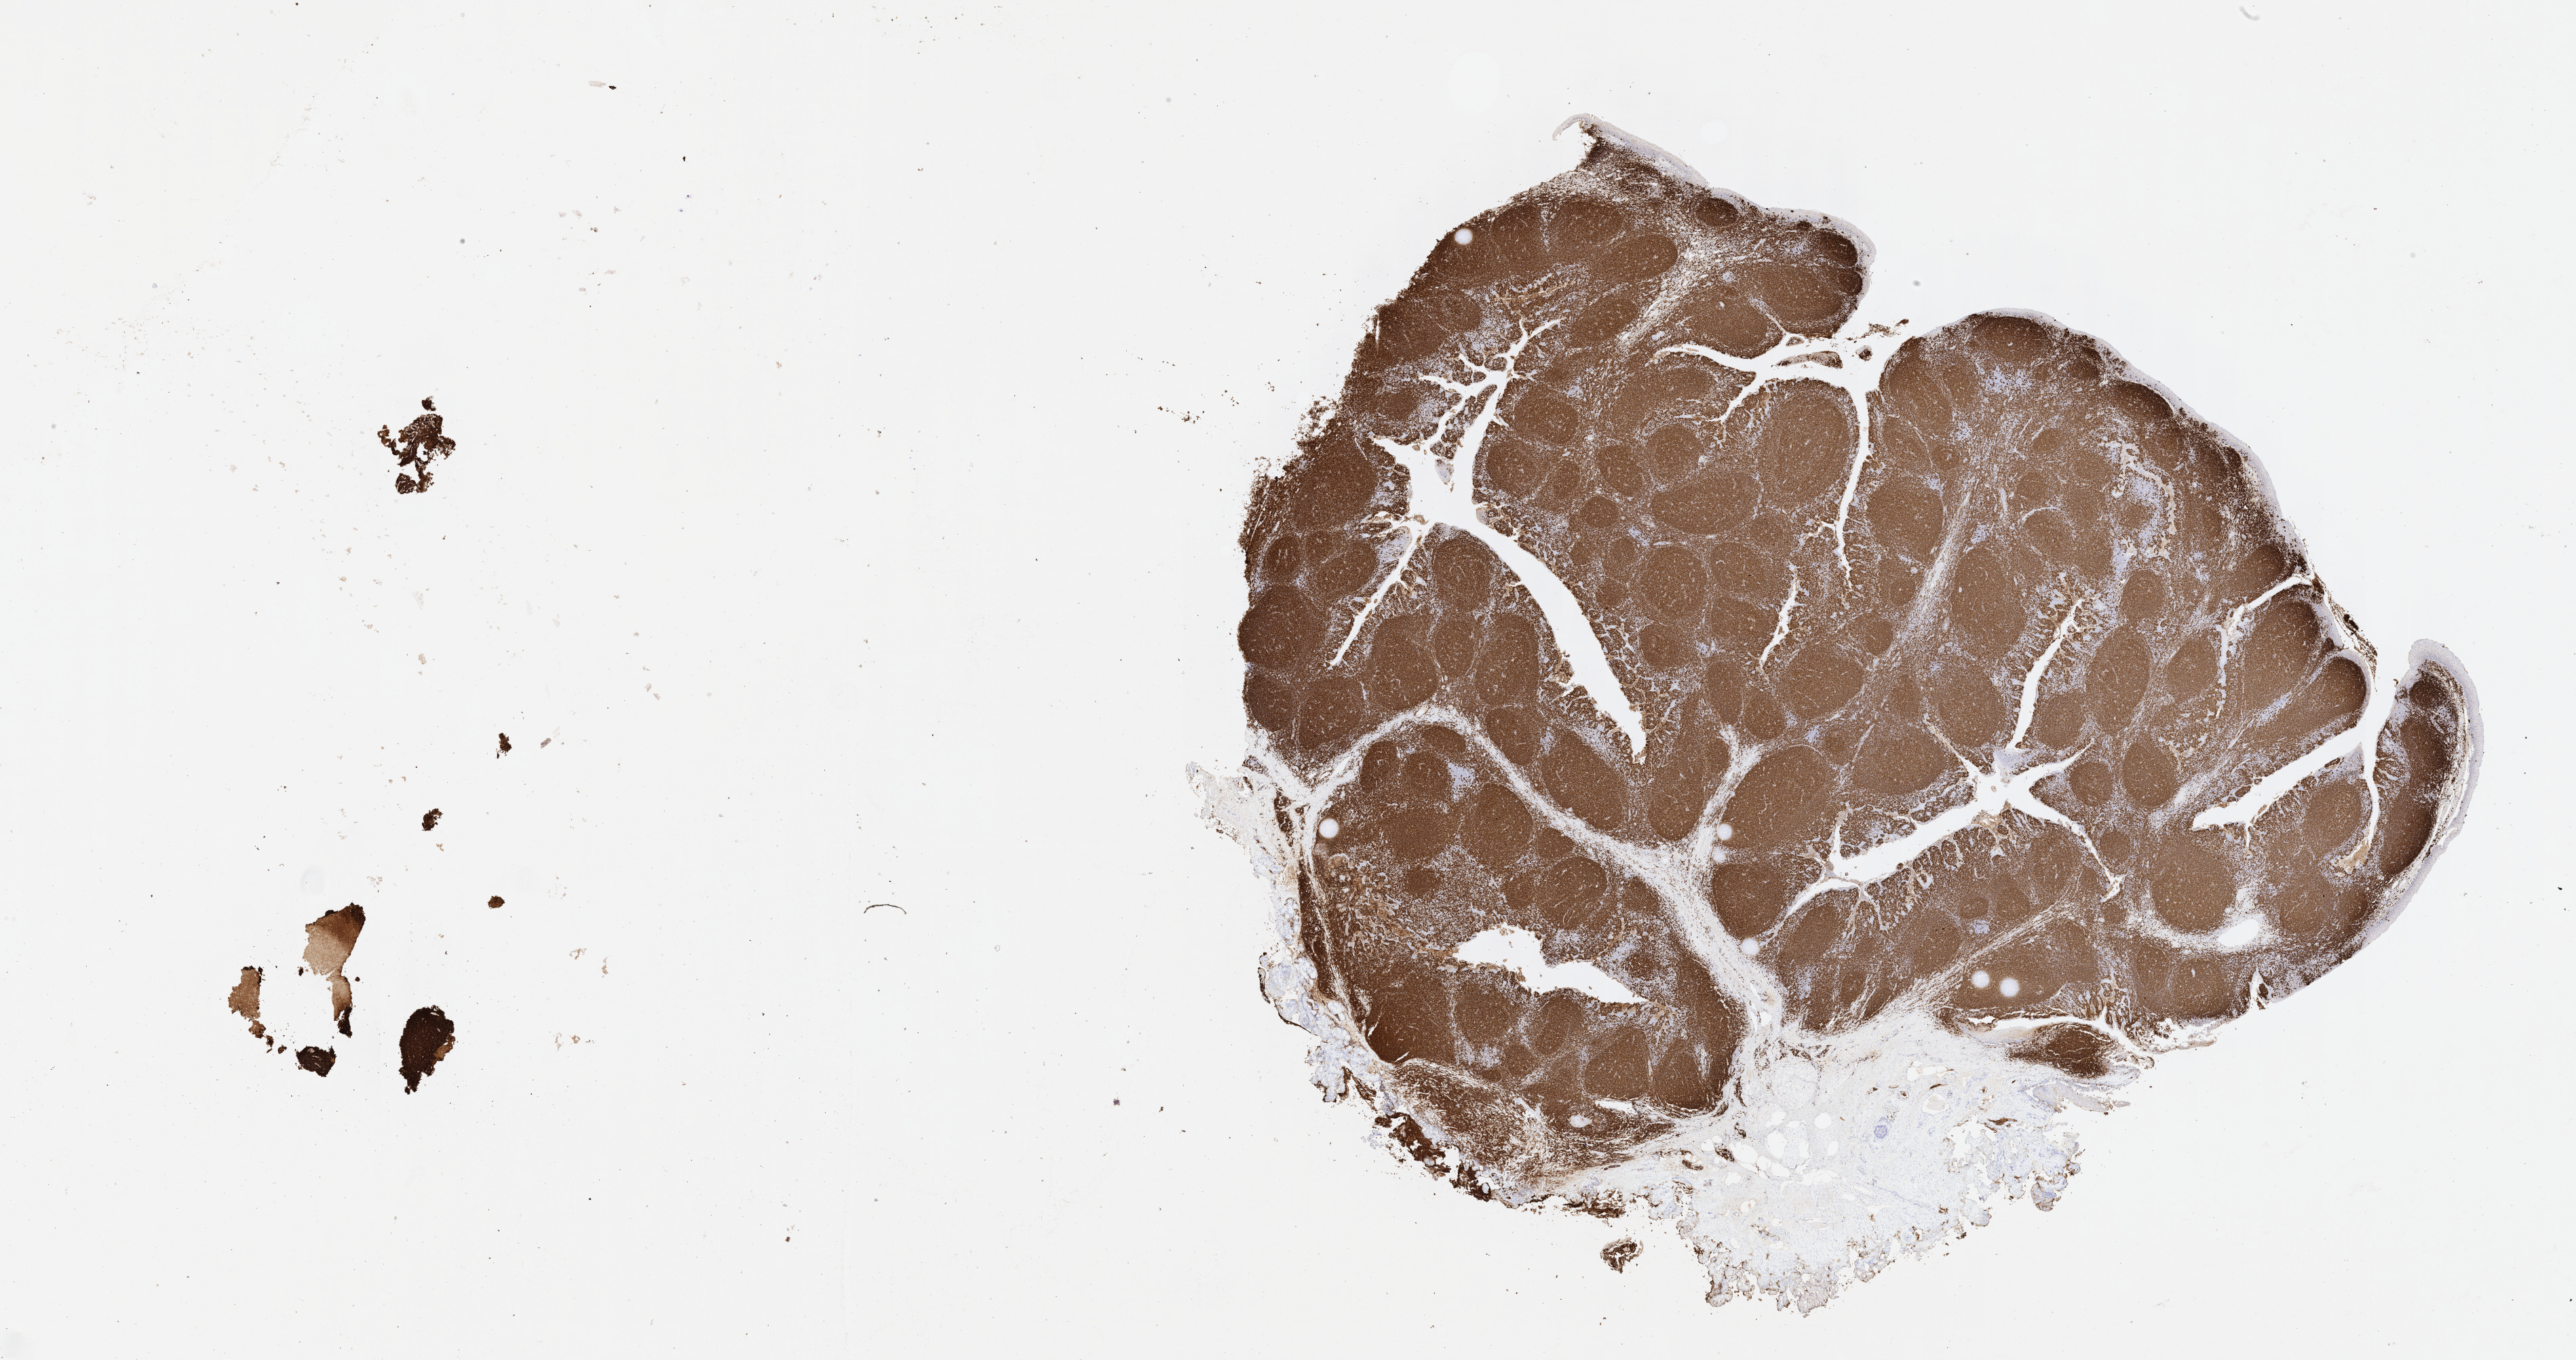
Whole-slide image, immunohistochemical stain for CD20 — shown as a low-resolution overview of the whole scanned area (about 30.7 x 16.2 mm); tumor tissue; site: abdominal lymph node. Male, age 5 years at initial diagnosis.
Histologic diagnosis: Diffuse large B-cell lymphoma, NOS.